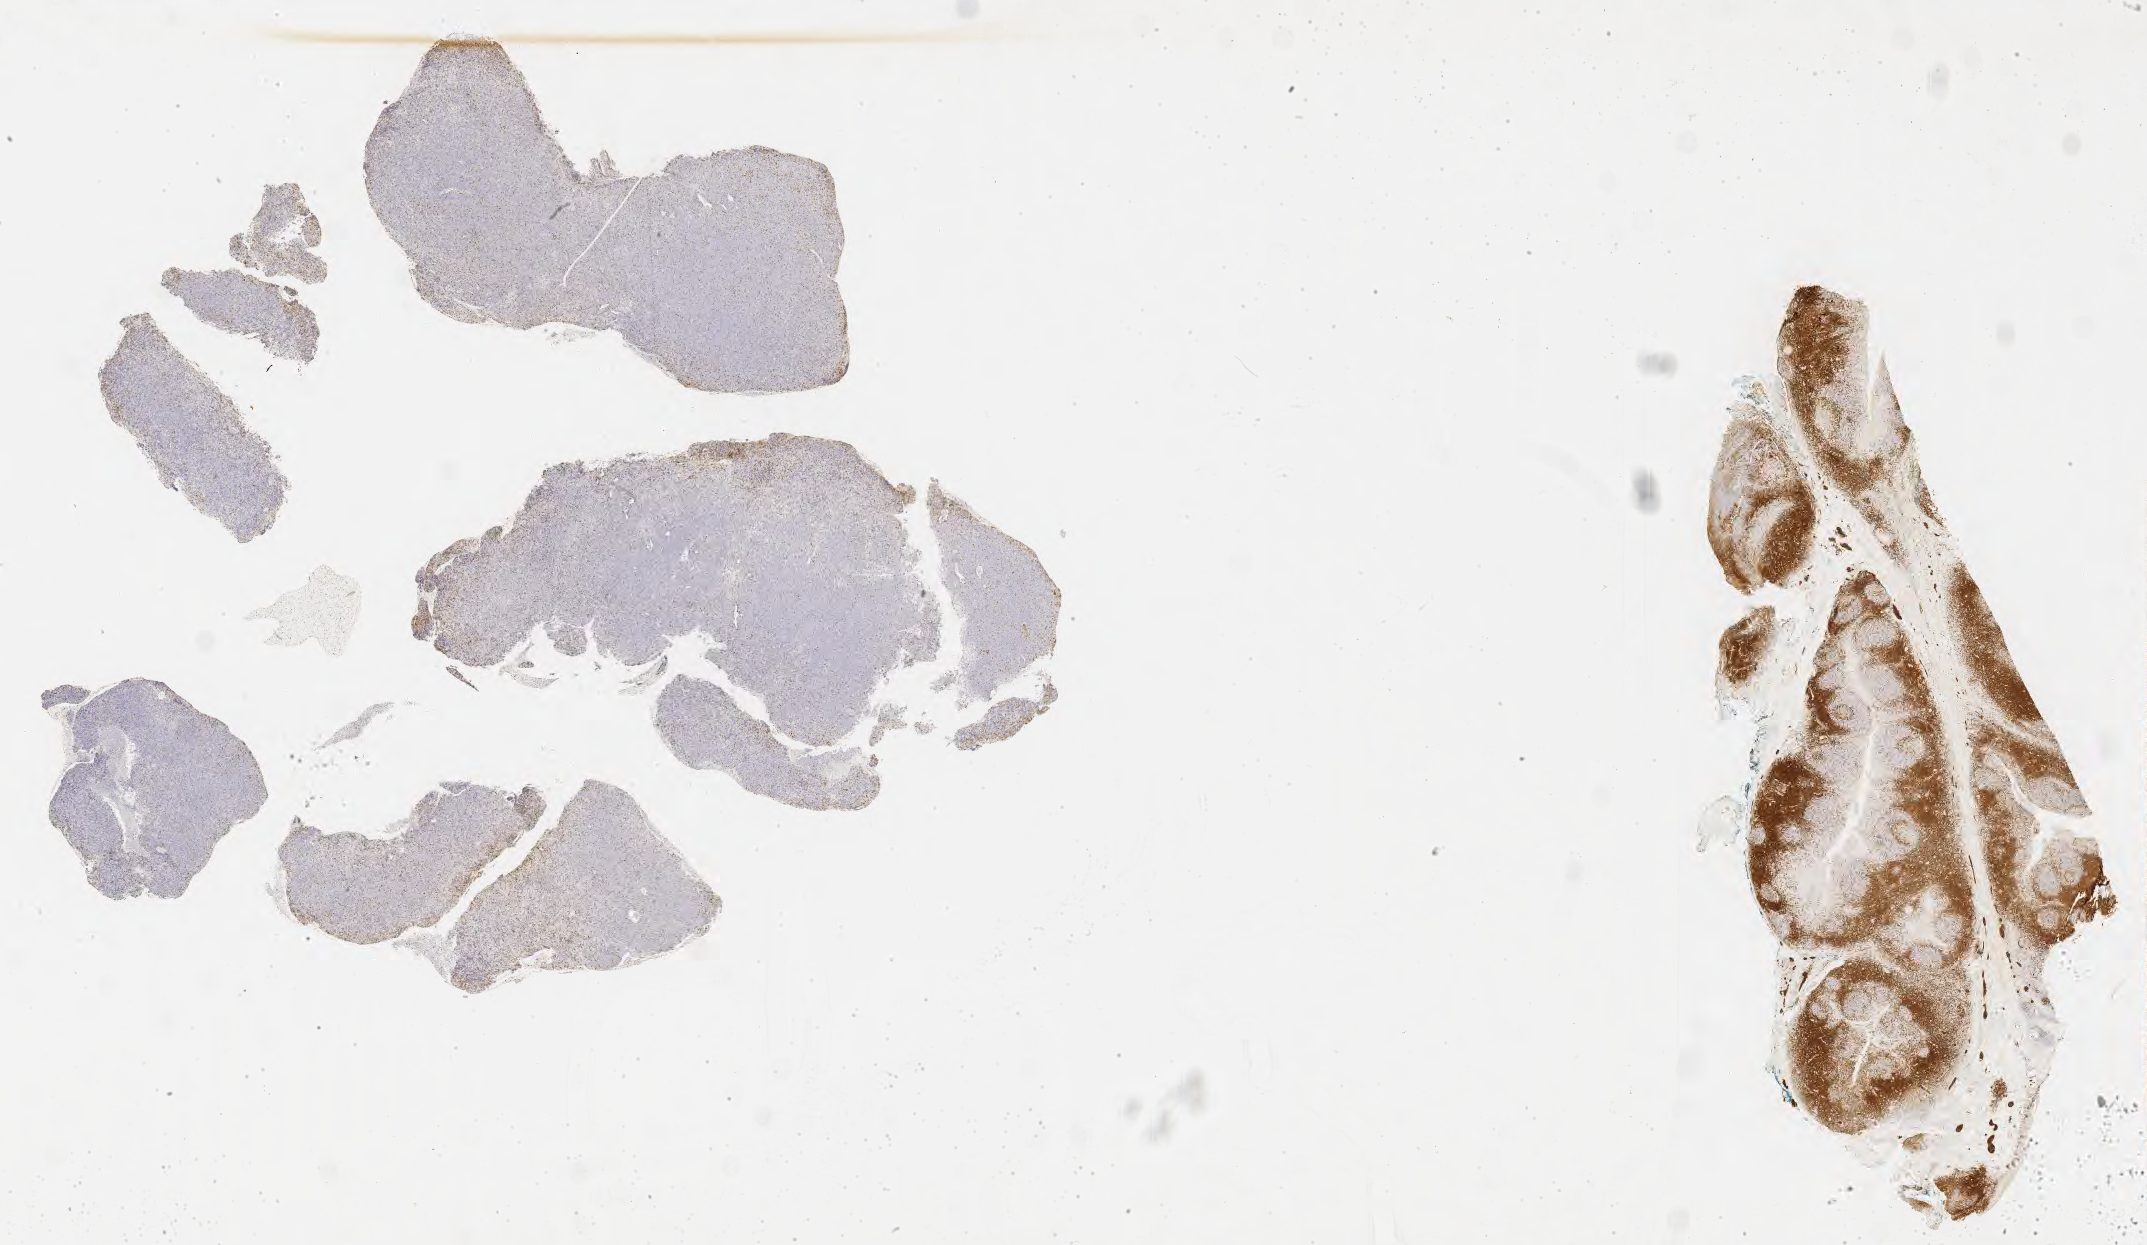
Whole-slide image, immunohistochemical stain for CD3 — low-resolution overview of the scanned area, about 34.7 x 20.1 mm. Tumor tissue. Site: soft tissue. Female patient; age at initial diagnosis 9 years.
Diagnosis: Burkitt lymphoma, NOS.